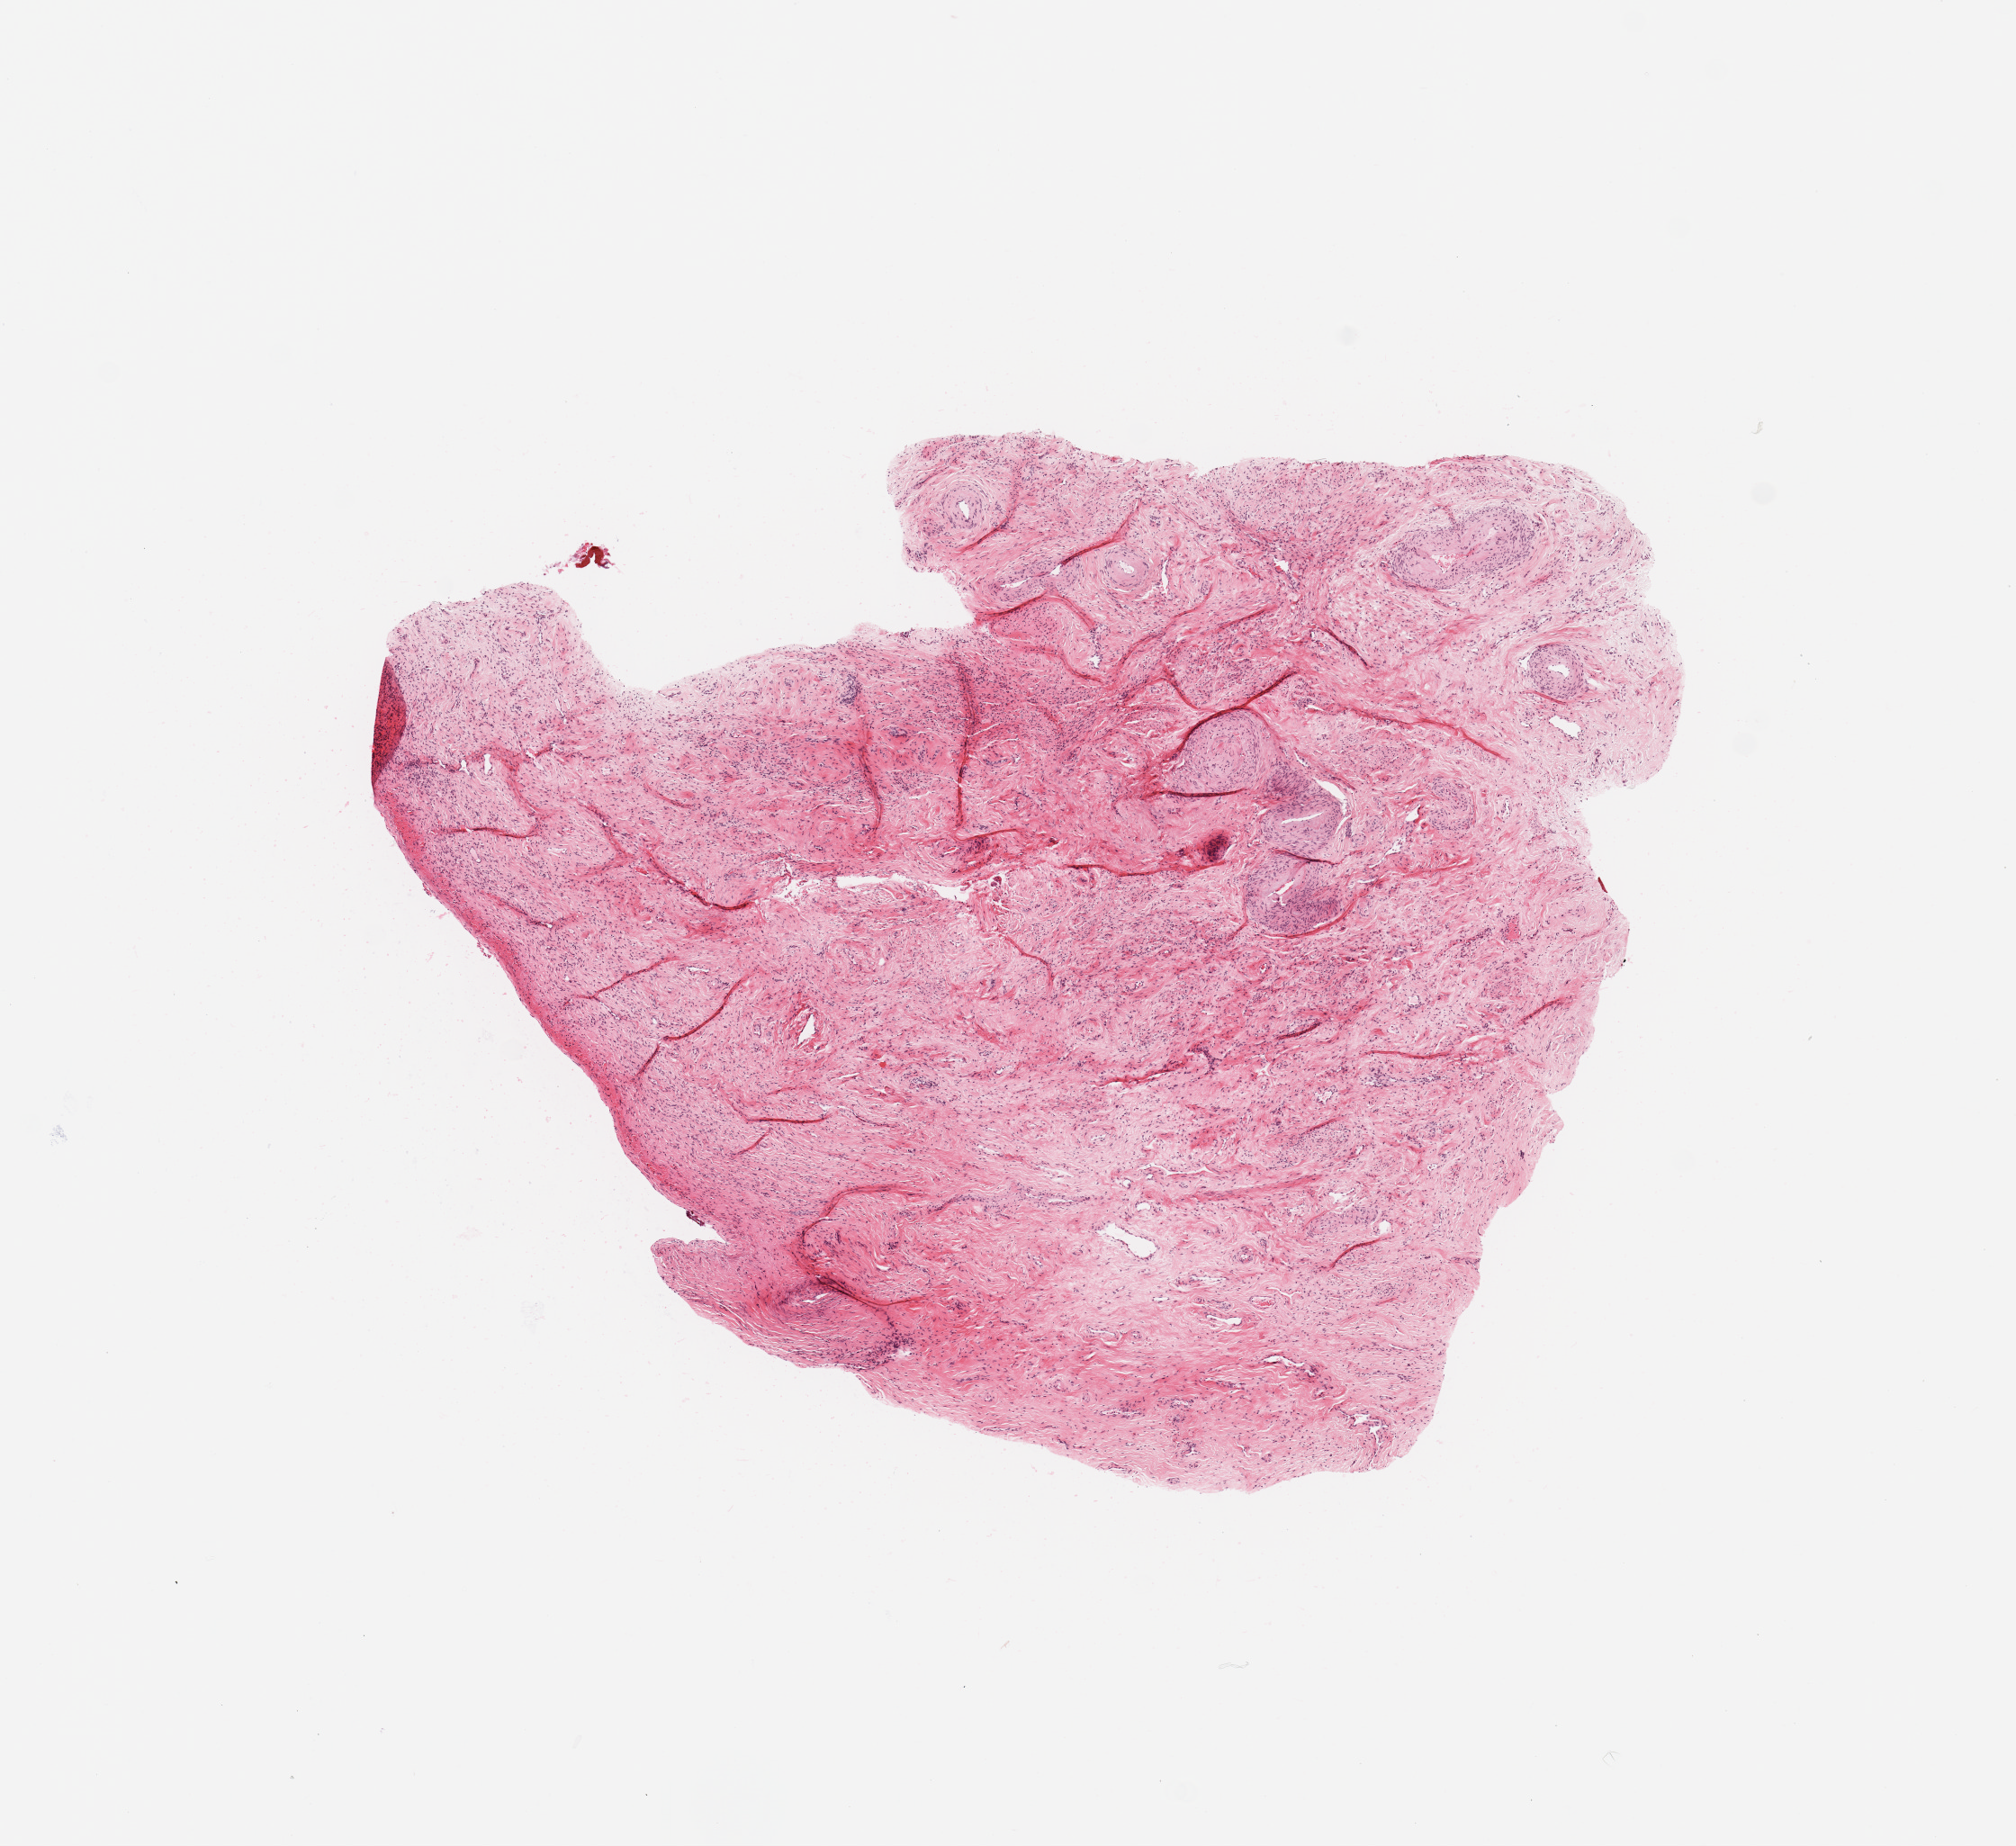
Whole-slide histology image, H&E, low-resolution overview of the scanned area, about 8.9 x 8.1 mm, uterus, normal (non-tumour) tissue. Patient: female, age 66 years.
- this section: normal (non-tumour) tissue from the same patient
- patient diagnosis: Endometrioid adenocarcinoma, NOS